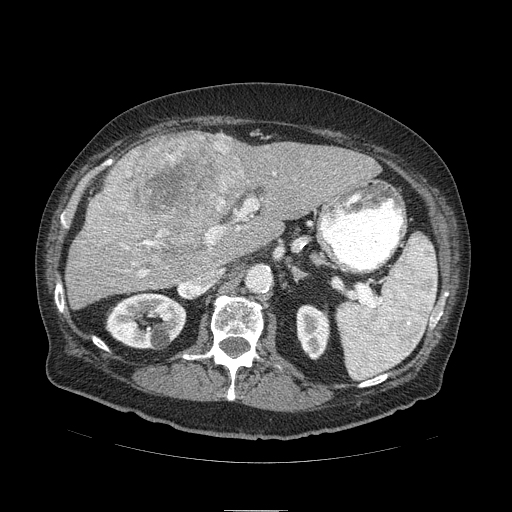
Contrast-enhanced abdominal CT (liver protocol), one axial slice. Slice 52 of 103 in the series (ordered by position). Soft-tissue window (W 400 / L 40 HU). 2.5 mm slice thickness. 512 × 512 image matrix, field of view 440 × 440 mm. Case-level facts recorded for this patient, not image findings: diagnosis: hepatocellular carcinoma (patient treated with transarterial chemoembolisation; whether this scan precedes or follows treatment is not stated here); TNM stage (as recorded): Stage-IIIA; Child-Pugh class: B; tumour nodularity: multinodular; tumour size: 13 cm.
Outlined on this slice (semi-automatically segmented with operator editing):
- liver parenchyma outside the tumour (the mass and vessels are separate outlines, so this box may not span the whole liver): bounding box [x1, y1, x2, y2] px = [64, 134, 380, 308]
- mass: [85, 130, 249, 254]
- liver vessels: [139, 173, 275, 277]